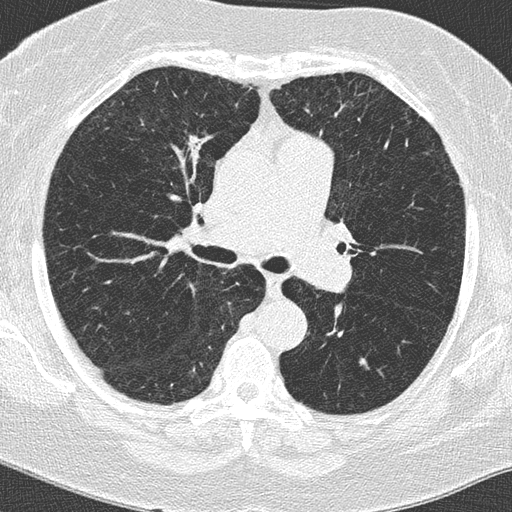
Axial slice from a low-dose chest CT screening exam, second annual screen, lung window (W 1500 / L -600 HU), 2 mm slice thickness, 512 × 512 image matrix. Female, age 62 years at enrolment.
Lesion marked by an expert reader, box from (x=159, y=114) to (x=225, y=179) px. The screening reader recorded 2 non-calcified nodules or masses ≥4 mm on this exam; which of them this box marks is not recorded. Later outcome: lung cancer diagnosed 396 days after this screen (after the third annual screen) — adenocarcinoma, NOS, right upper lobe, moderately differentiated (G2), stage IA (AJCC 6th edition), 15 mm at pathology.